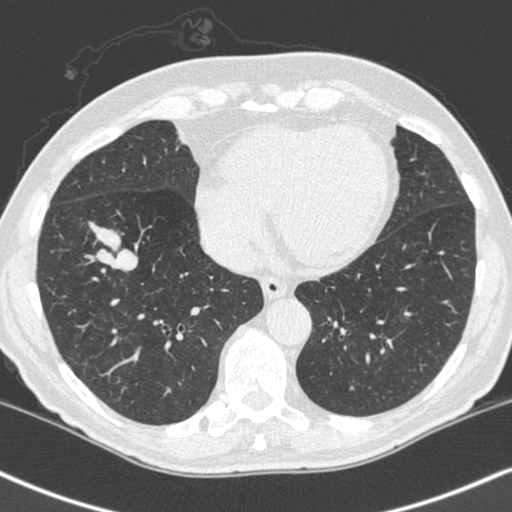
Low-dose screening chest CT, axial slice; baseline annual screen; lung window (W 1500 / L -600 HU); slice 158 of 248 in the series. Male participant, aged 68 years at enrolment. Current smoker at enrolment.
Expert reader's lesion annotation, bounding box [x1, y1, x2, y2] px = [78, 205, 153, 274]. Reader record for this screening exam (exam-level; its link to the box is not recorded): non-calcified nodule or mass ≥4 mm, right lower lobe, 34 × 17 mm, smooth margins, soft tissue attenuation. Participant outcome: lung cancer diagnosed 24 days after this screen — combined small cell carcinoma, right lower lobe, stage IIIA (AJCC 6th edition), 41 mm at pathology.